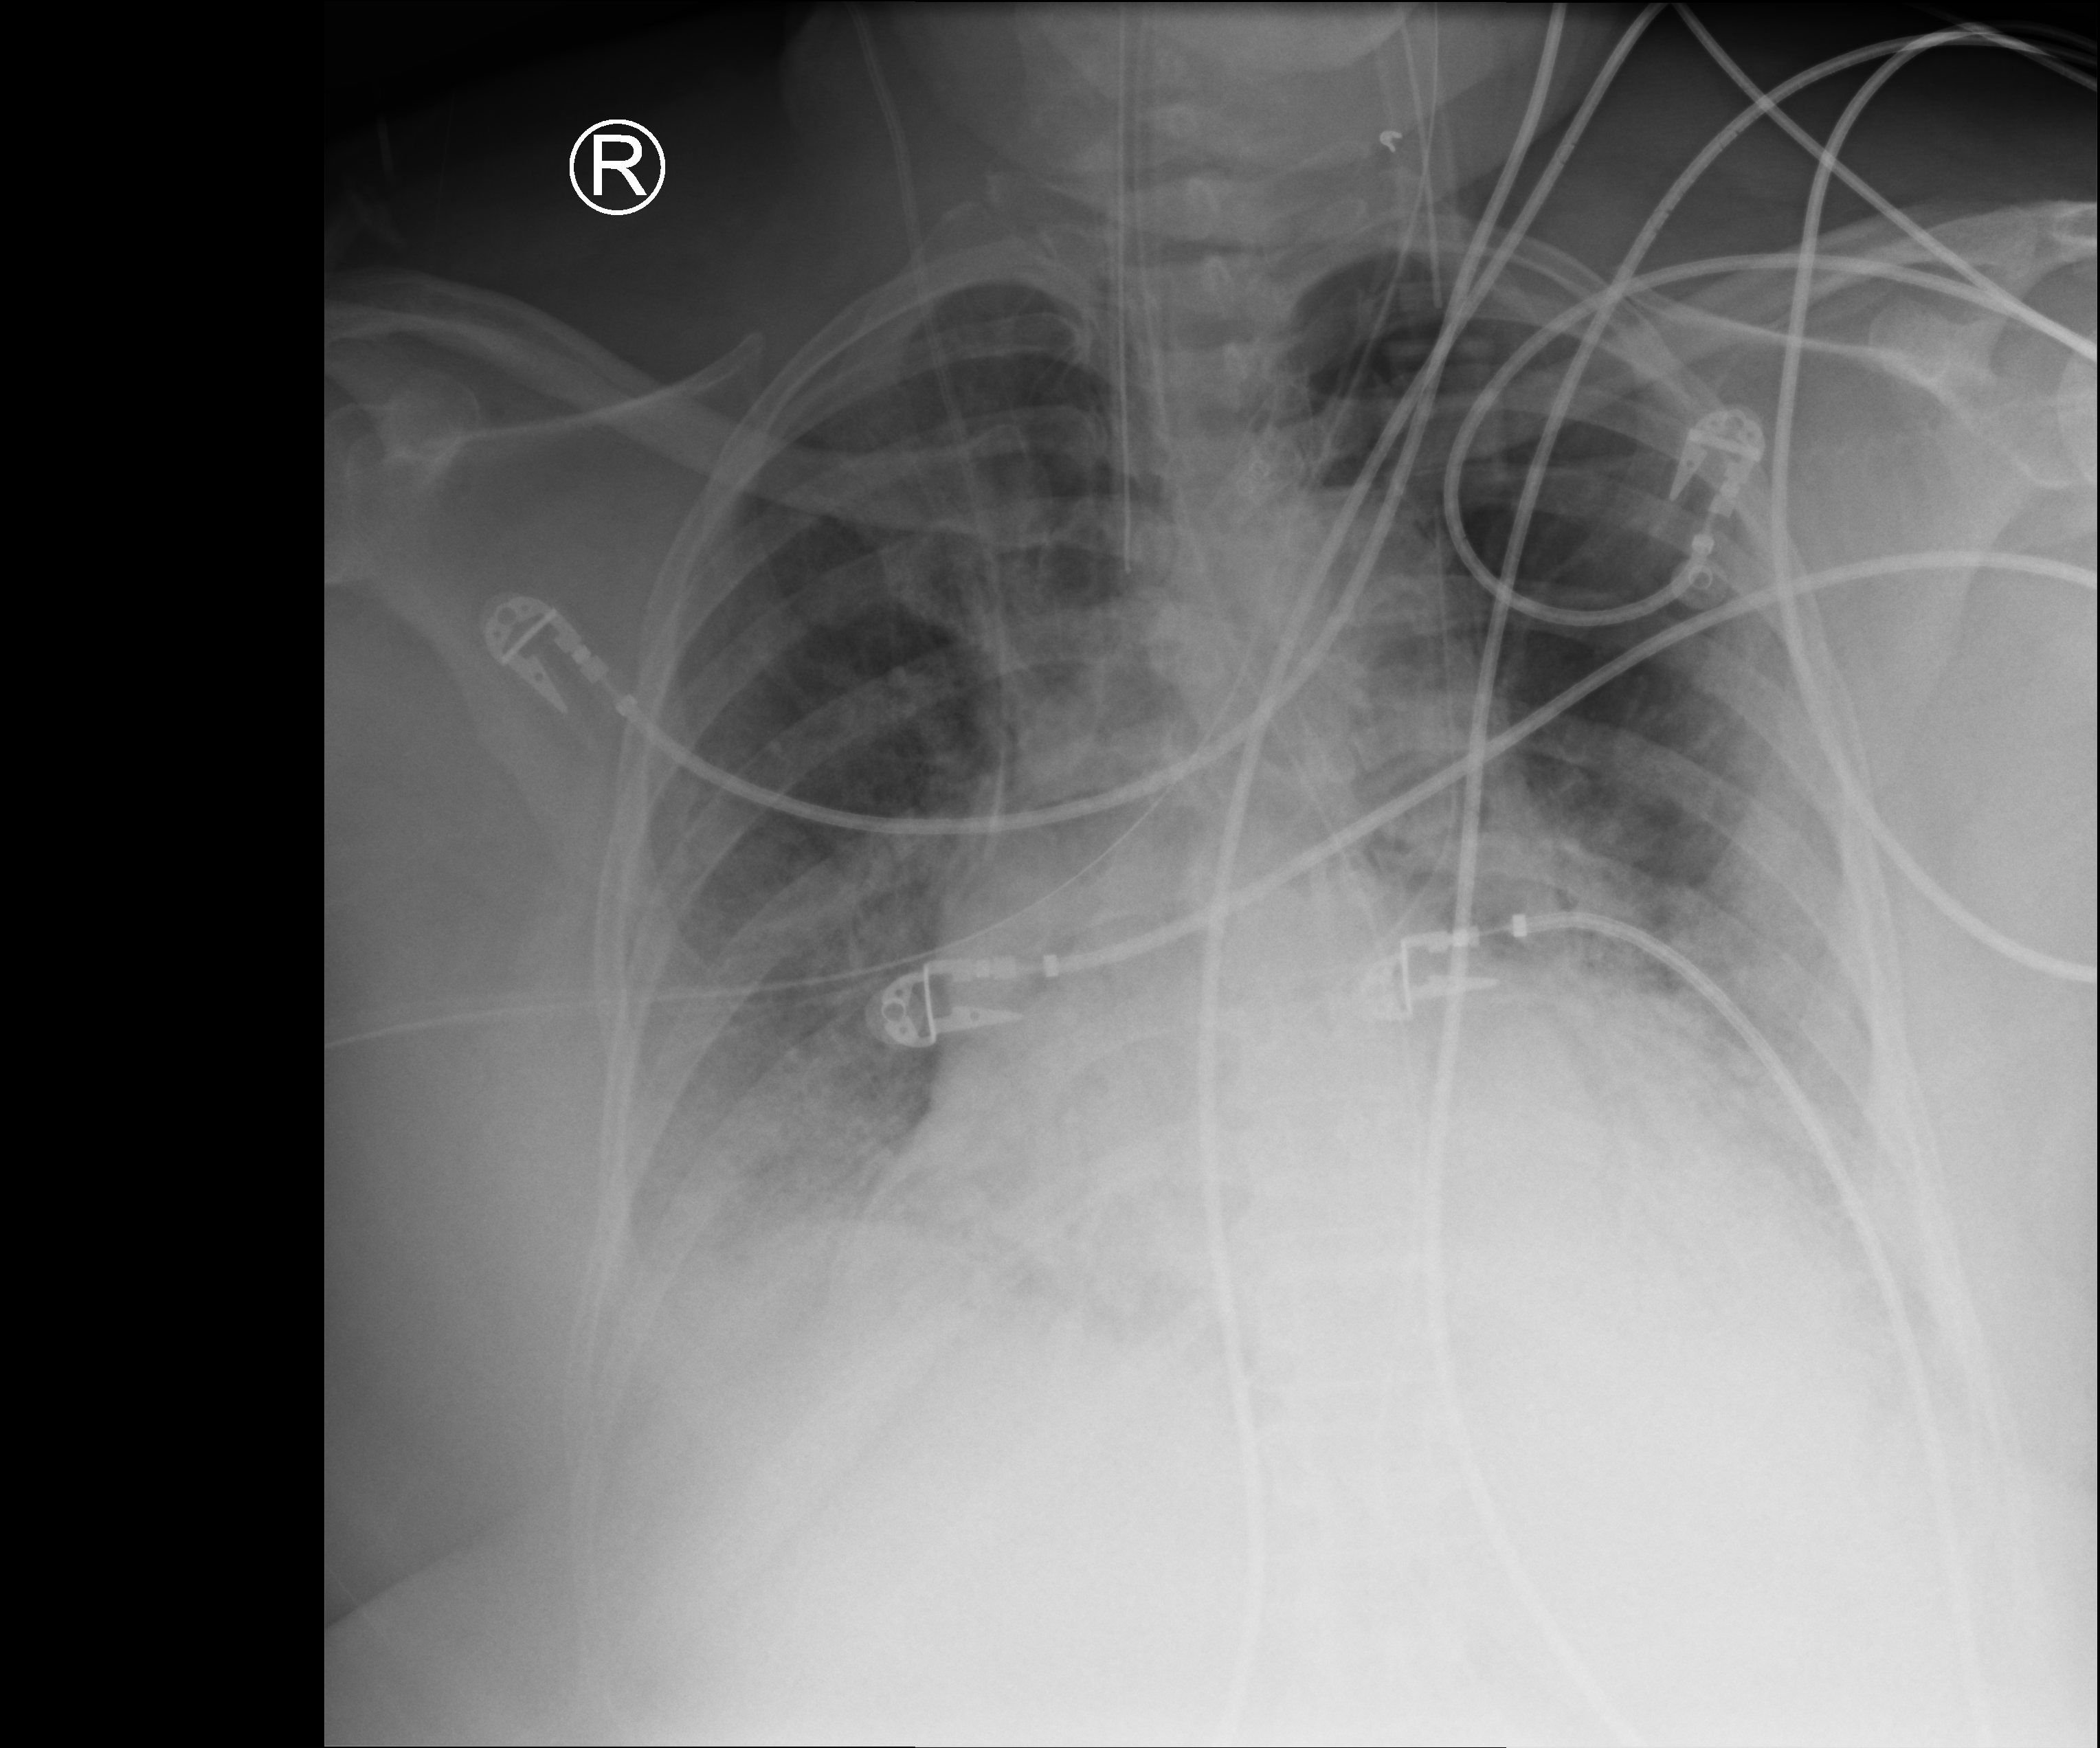
Portable chest radiograph; anteroposterior (AP) projection. Female patient hospitalised with COVID-19, age 60–74 years.
Admission-level facts for this patient (not findings on this image; timing relative to this image not recorded): mechanically ventilated during this hospital stay: yes.